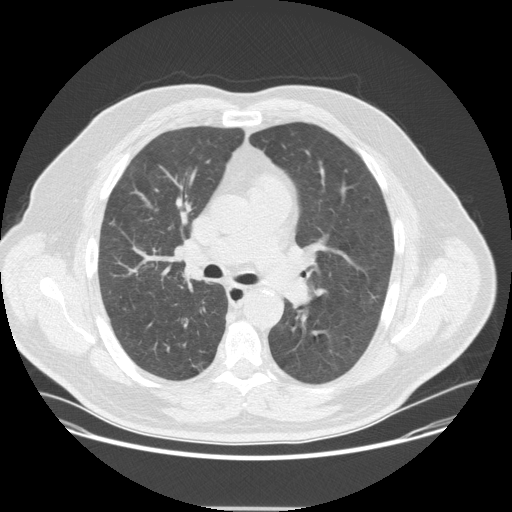
Low-dose screening chest CT, one axial slice. Position 218 of 351 along the scan axis. Reconstruction kernel STANDARD. 120 kVp. Lung window (W 1500 / L -600 HU). 2.5 mm slice thickness. 512 × 512 image matrix.
Outlined on this slice (expert manual segmentation):
- lesion 1 (tumor, upper lobe of right lung): box from (x=182, y=273) to (x=194, y=281) px